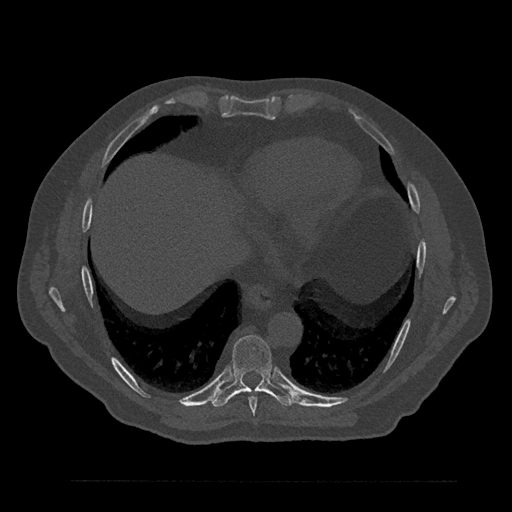
CT including the spine, one axial slice; slice 421 of 797 in the series (ordered by position); 120 kVp; bone window (W 1800 / L 400 HU); 0.5 mm slice thickness; 512 × 512 image matrix. Patient: male, 61 years. Case-level facts recorded for this patient, not image findings: primary cancer: prostate.
Outlined on this slice (semi-automatically segmented with operator editing):
- T8 vertebra: bounding box (x1, y1, x2, y2) in pixels: (249, 397, 258, 416)
- T9 vertebra: (212, 335, 295, 407)